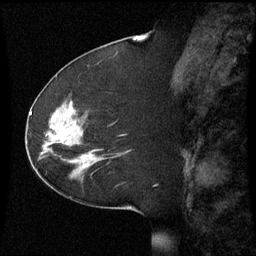
Breast MRI (dynamic contrast-enhanced), one sagittal slice; slice 28 of 60 in the series (ordered by position); dynamic contrast-enhanced series, image 2 of 3 at this slice position (ordered by acquisition); 1.5 T; TE 4.2 ms, TR 8.9 ms; 2.2 mm slice thickness; 256 × 256 image matrix, field of view 220 × 220 mm. Patient: female, 51 years. Case-level facts recorded for this patient, not image findings: setting: breast cancer imaged before/during neoadjuvant chemotherapy; receptor status: HR-positive, HER2-negative.
Structures marked on this image (semi-automatic segmentation, software-assisted and operator-edited):
- analysis volume of interest (the breast-tissue region the enhancement analysis was run in; not a lesion): bounding box <44,102,105,169> (left, top, right, bottom; pixels)
- tumour enhancement mask (voxels above the 70 % enhancement threshold inside the analysis volume of interest): <52,126,91,157>